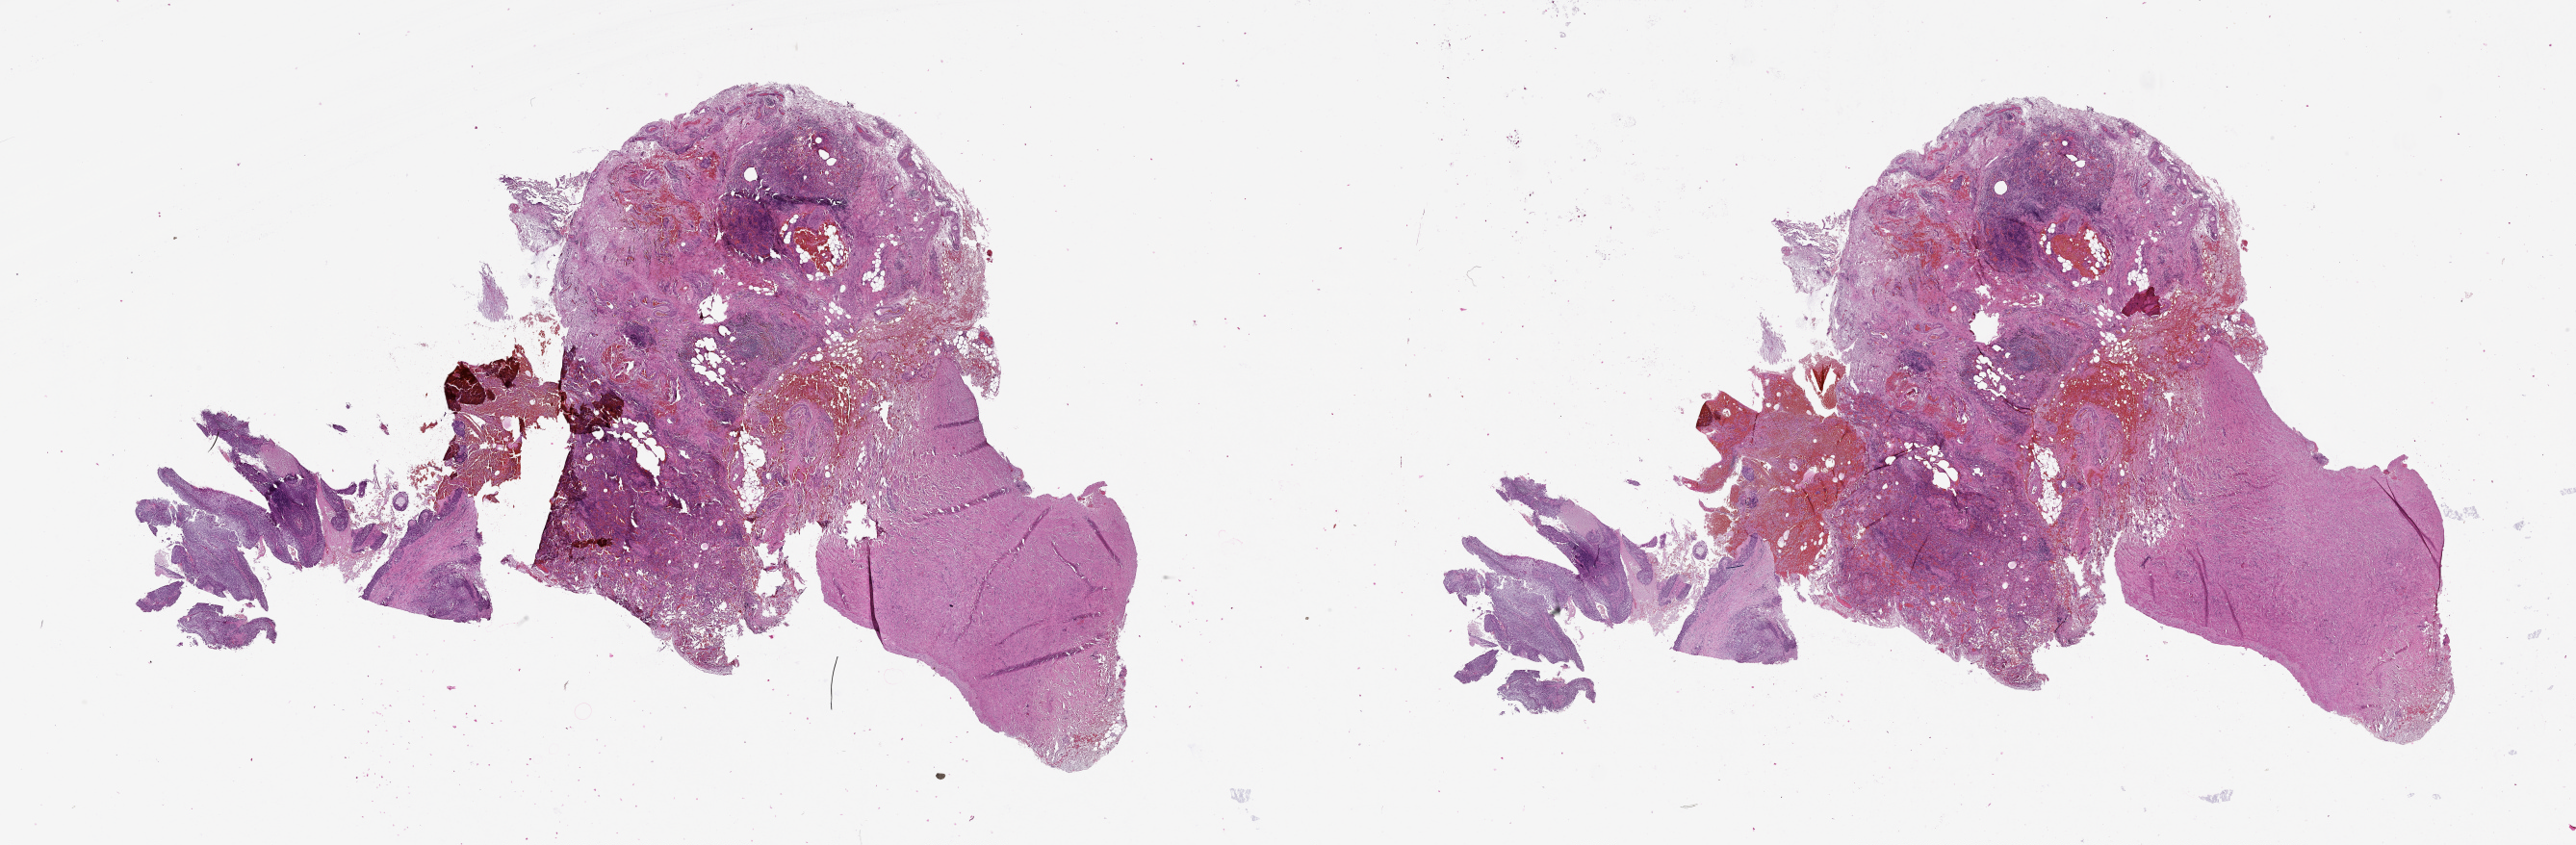
Whole-slide histology image, H&E, shown as a low-resolution overview of the whole scanned area (about 43.1 x 14.1 mm, from a 20x scan). Tumour tissue sample, lung. Male, 58 y/o.
Patient diagnosis (cohort enrolment): squamous cell carcinoma (lung).